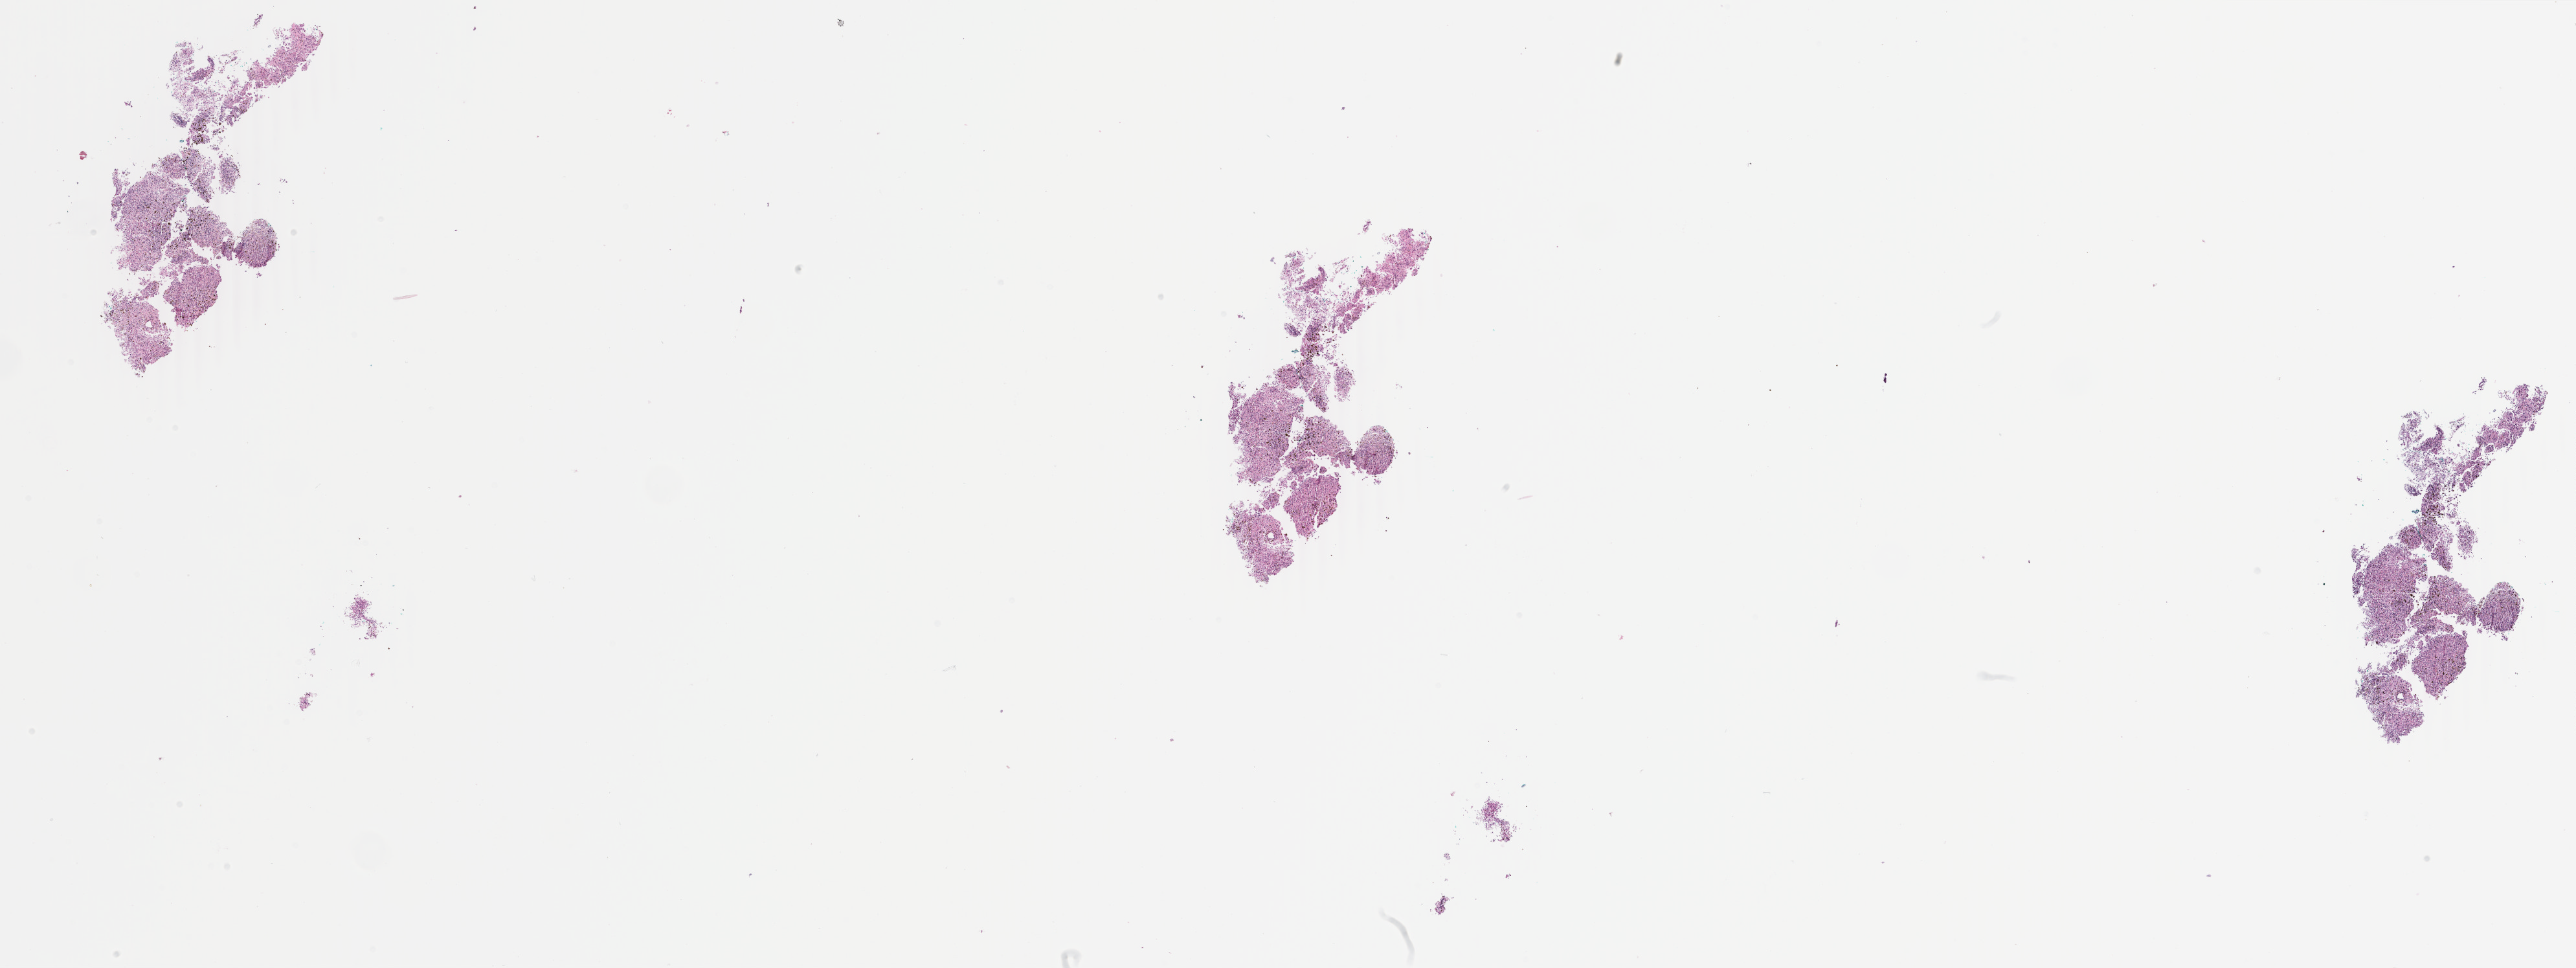
Whole-slide histology image, H&E, a low-resolution overview of the entire scanned area, about 31.6 x 11.9 mm, FFPE section, skin, primary tumour sample. Female patient; age at initial diagnosis 83 years.
Histologic diagnosis: Malignant melanoma, NOS.